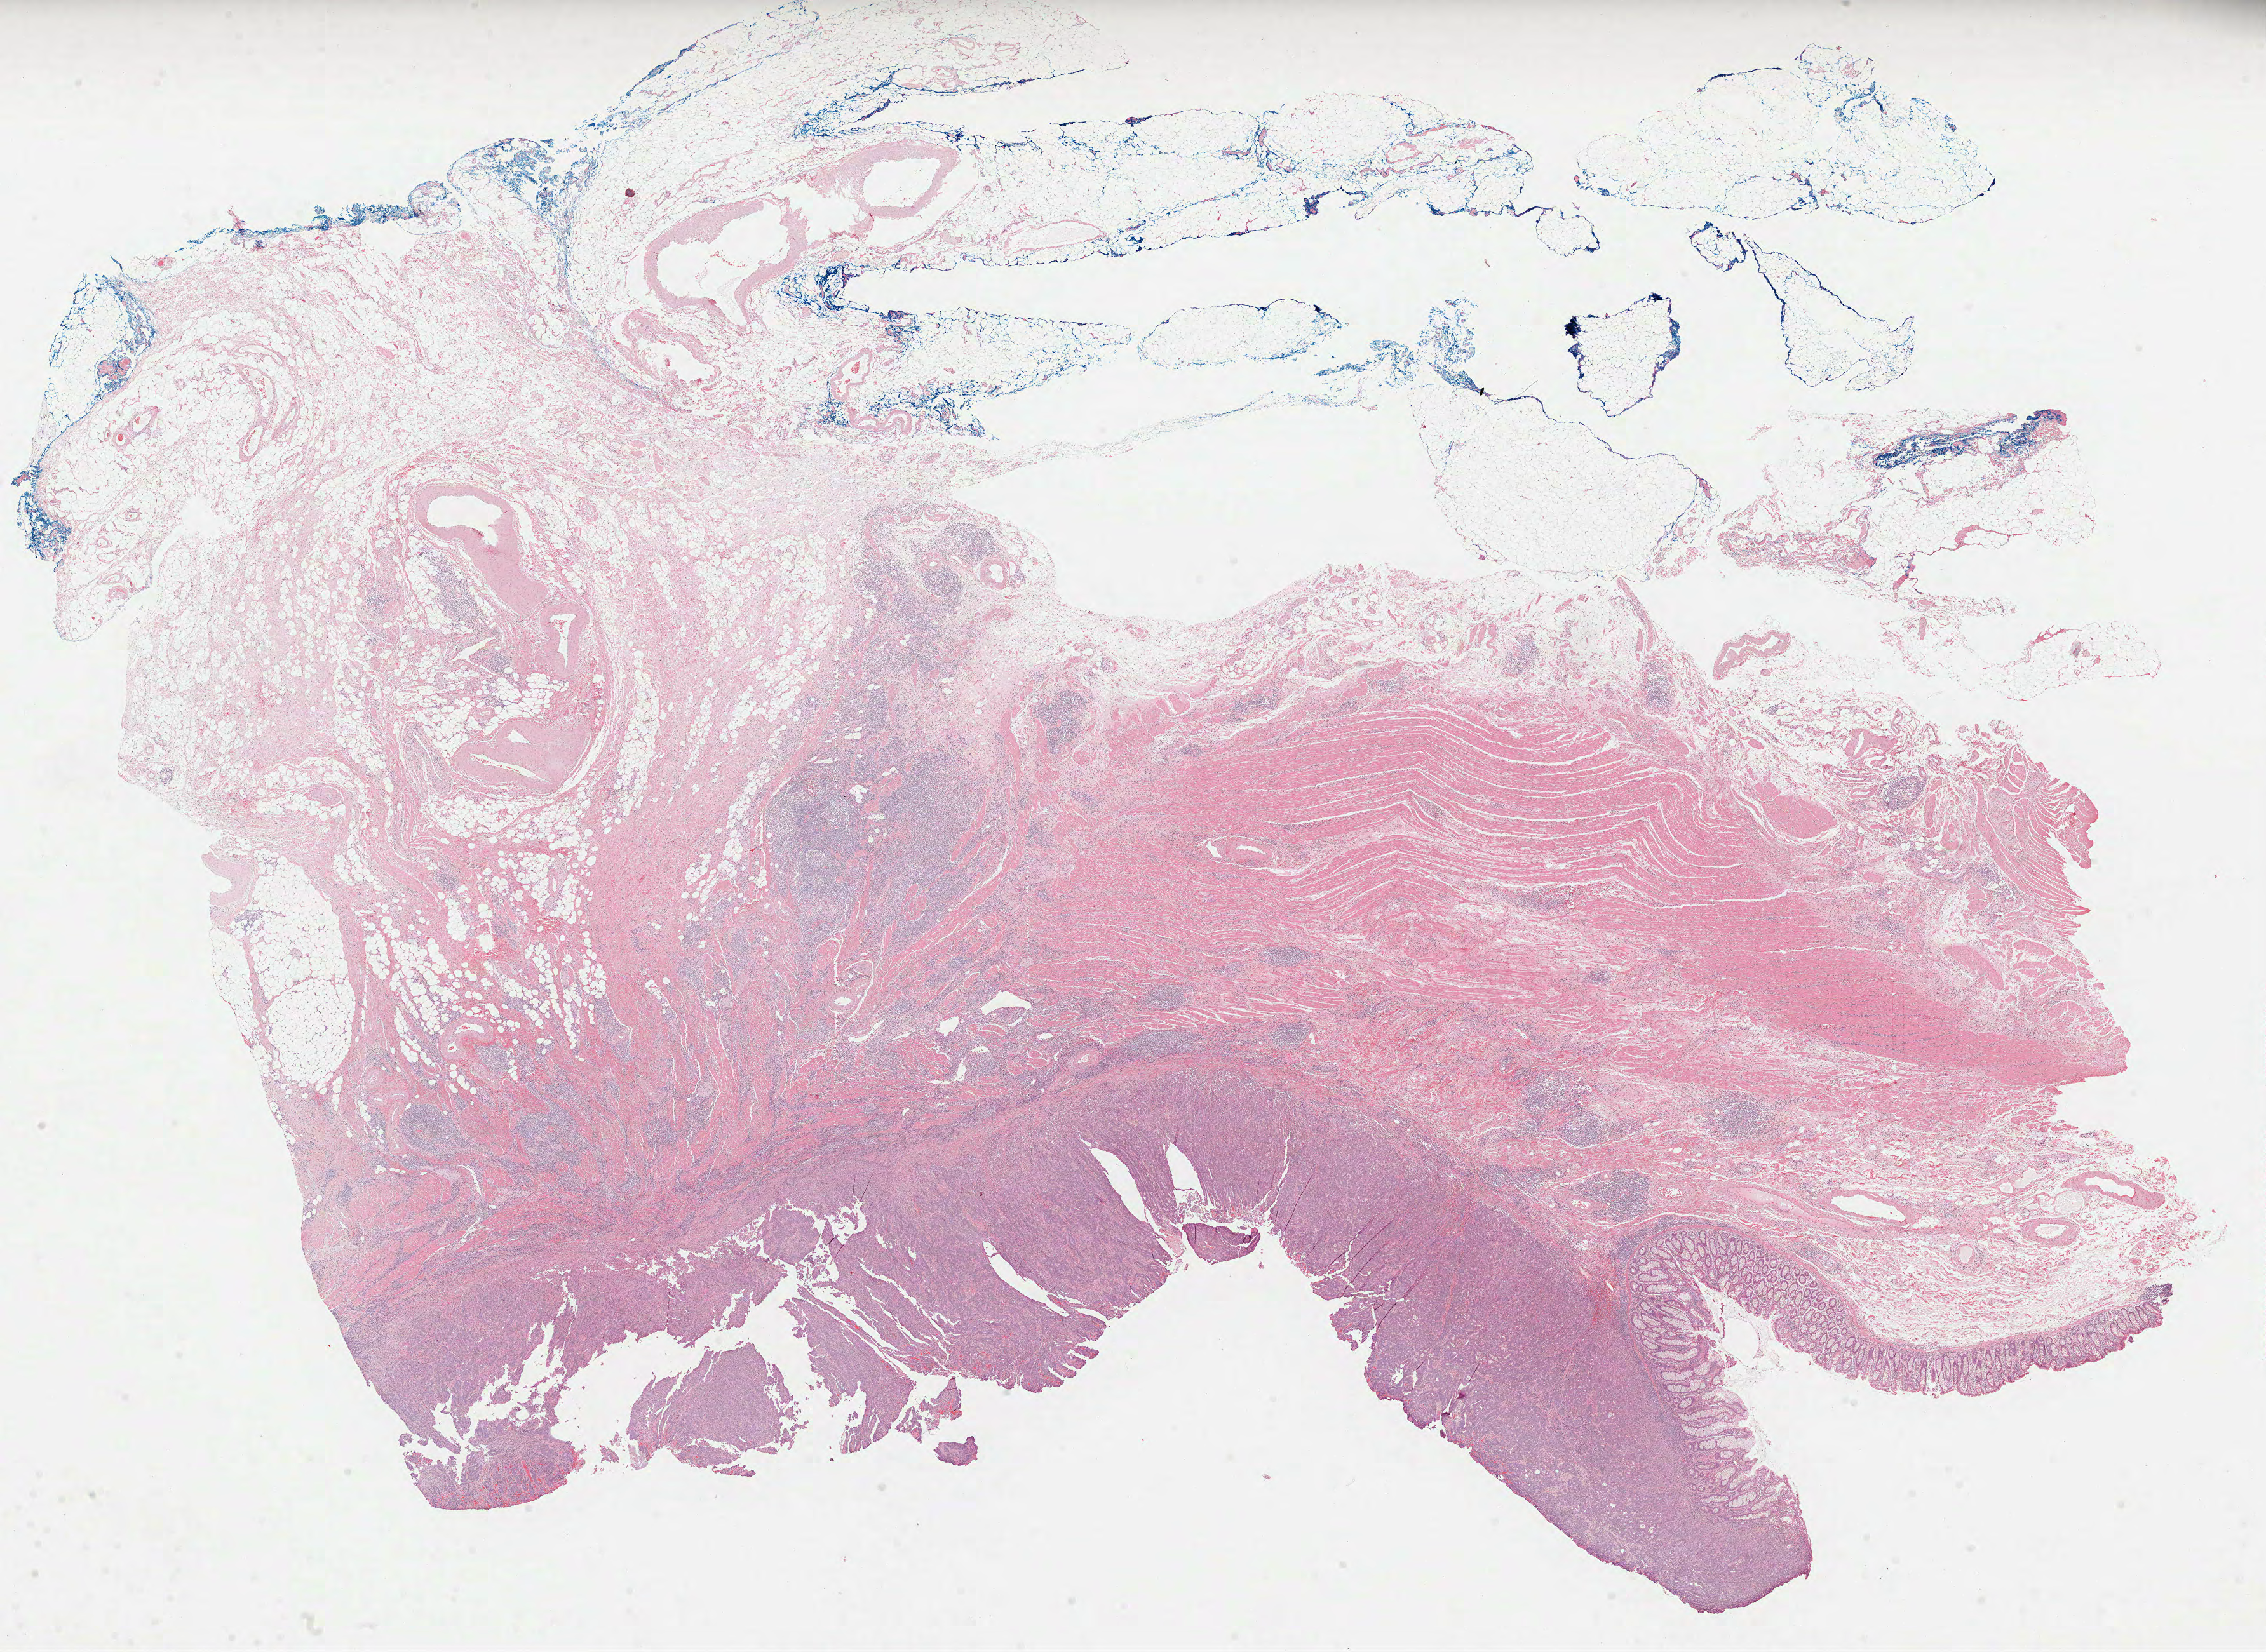
Digitized H&E-stained tissue section (whole slide) — low-resolution overview of the scanned area, about 28.8 x 21.0 mm (slide scanned at 40x); formalin-fixed paraffin-embedded (FFPE) diagnostic section; primary tumour sample from the colon. Male patient; age at initial diagnosis 78 years.
- AJCC pathologic stage: I (6th edition)
- diagnosis: Adenocarcinoma, NOS (cecum)
- lymph nodes positive (case pathology): 0 of 16 examined